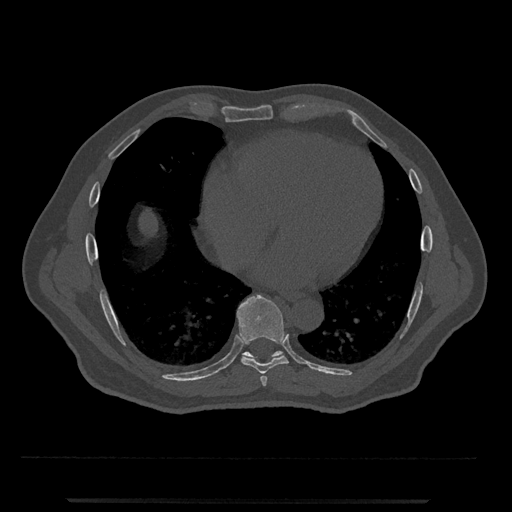
CT including the spine, one axial slice. Slice 615 of 797 in the series (ordered by position). Bone window (W 1800 / L 400 HU). 0.5 mm slice thickness. 512 × 512 image matrix, field of view 419 × 419 mm. Patient: male, 63 years. Case-level facts recorded for this patient, not image findings: primary cancer: prostate.
Structures marked on this image (semi-automatic segmentation, software-assisted and operator-edited):
- T7 vertebra: bounding box (x1, y1, x2, y2) in pixels: (260, 375, 268, 386)
- T8 vertebra: (237, 295, 289, 374)
- T9 vertebra: (242, 351, 283, 362)